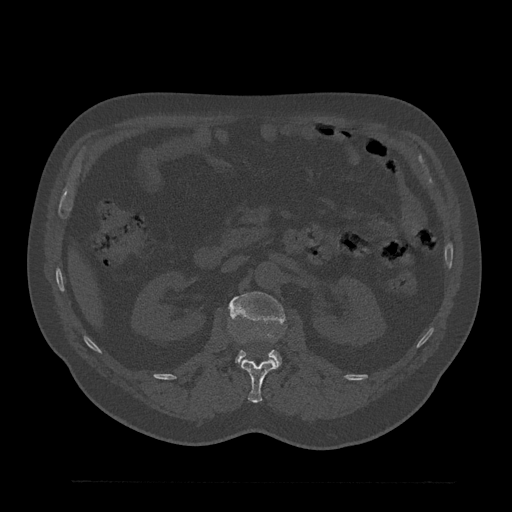
CT including the spine, one axial slice; slice 135 of 797 in the series (ordered by position); reconstruction kernel Br40s/3; 120 kVp; bone window (W 1800 / L 400 HU); 0.5 mm slice thickness; 512 × 512 image matrix, field of view 430 × 430 mm. Patient: male, 61 years. Case-level facts recorded for this patient, not image findings: primary cancer: prostate.
Outlined on this slice (semi-automatic segmentation, software-assisted and operator-edited):
- L1 vertebra: bounding box [x1, y1, x2, y2] px = [241, 360, 276, 403]
- L2 vertebra: [228, 292, 285, 366]